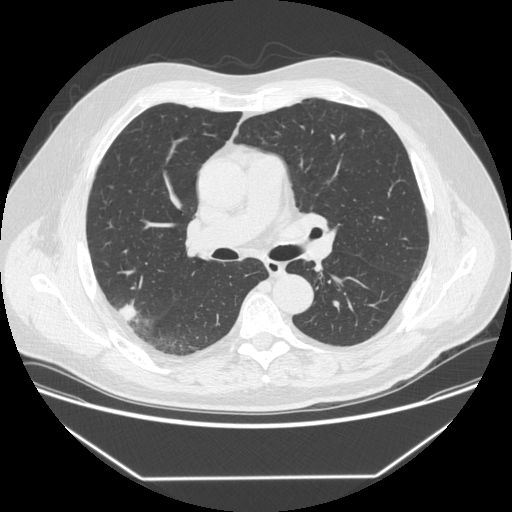
Low-dose screening chest CT, axial slice; first (baseline) screen; lung window (W 1500 / L -600 HU); 1.25 mm slice thickness; 120 kVp; 512 × 512 image matrix, field of view 410 × 410 mm. Male participant, aged 64 years at enrolment. Former smoker at enrolment.
Expert-annotated lung lesion, bounding box [x1, y1, x2, y2] px = [102, 299, 144, 333]. The exam's reader record, not a measurement of the box and not confirmed to be the same lesion: non-calcified nodule or mass ≥4 mm, right upper lobe, 12 × 12 mm, smooth margins, soft tissue attenuation. Official screen result: positive, change unspecified: nodule(s) >= 4 mm or enlarging nodule(s), mass(es), or other non-specific abnormalities suspicious for lung cancer. Participant outcome: lung cancer diagnosed 92 days after this screen — adenocarcinoma, NOS, right upper lobe, poorly differentiated (G3), stage IIIB (AJCC 6th edition), 15 mm at pathology.